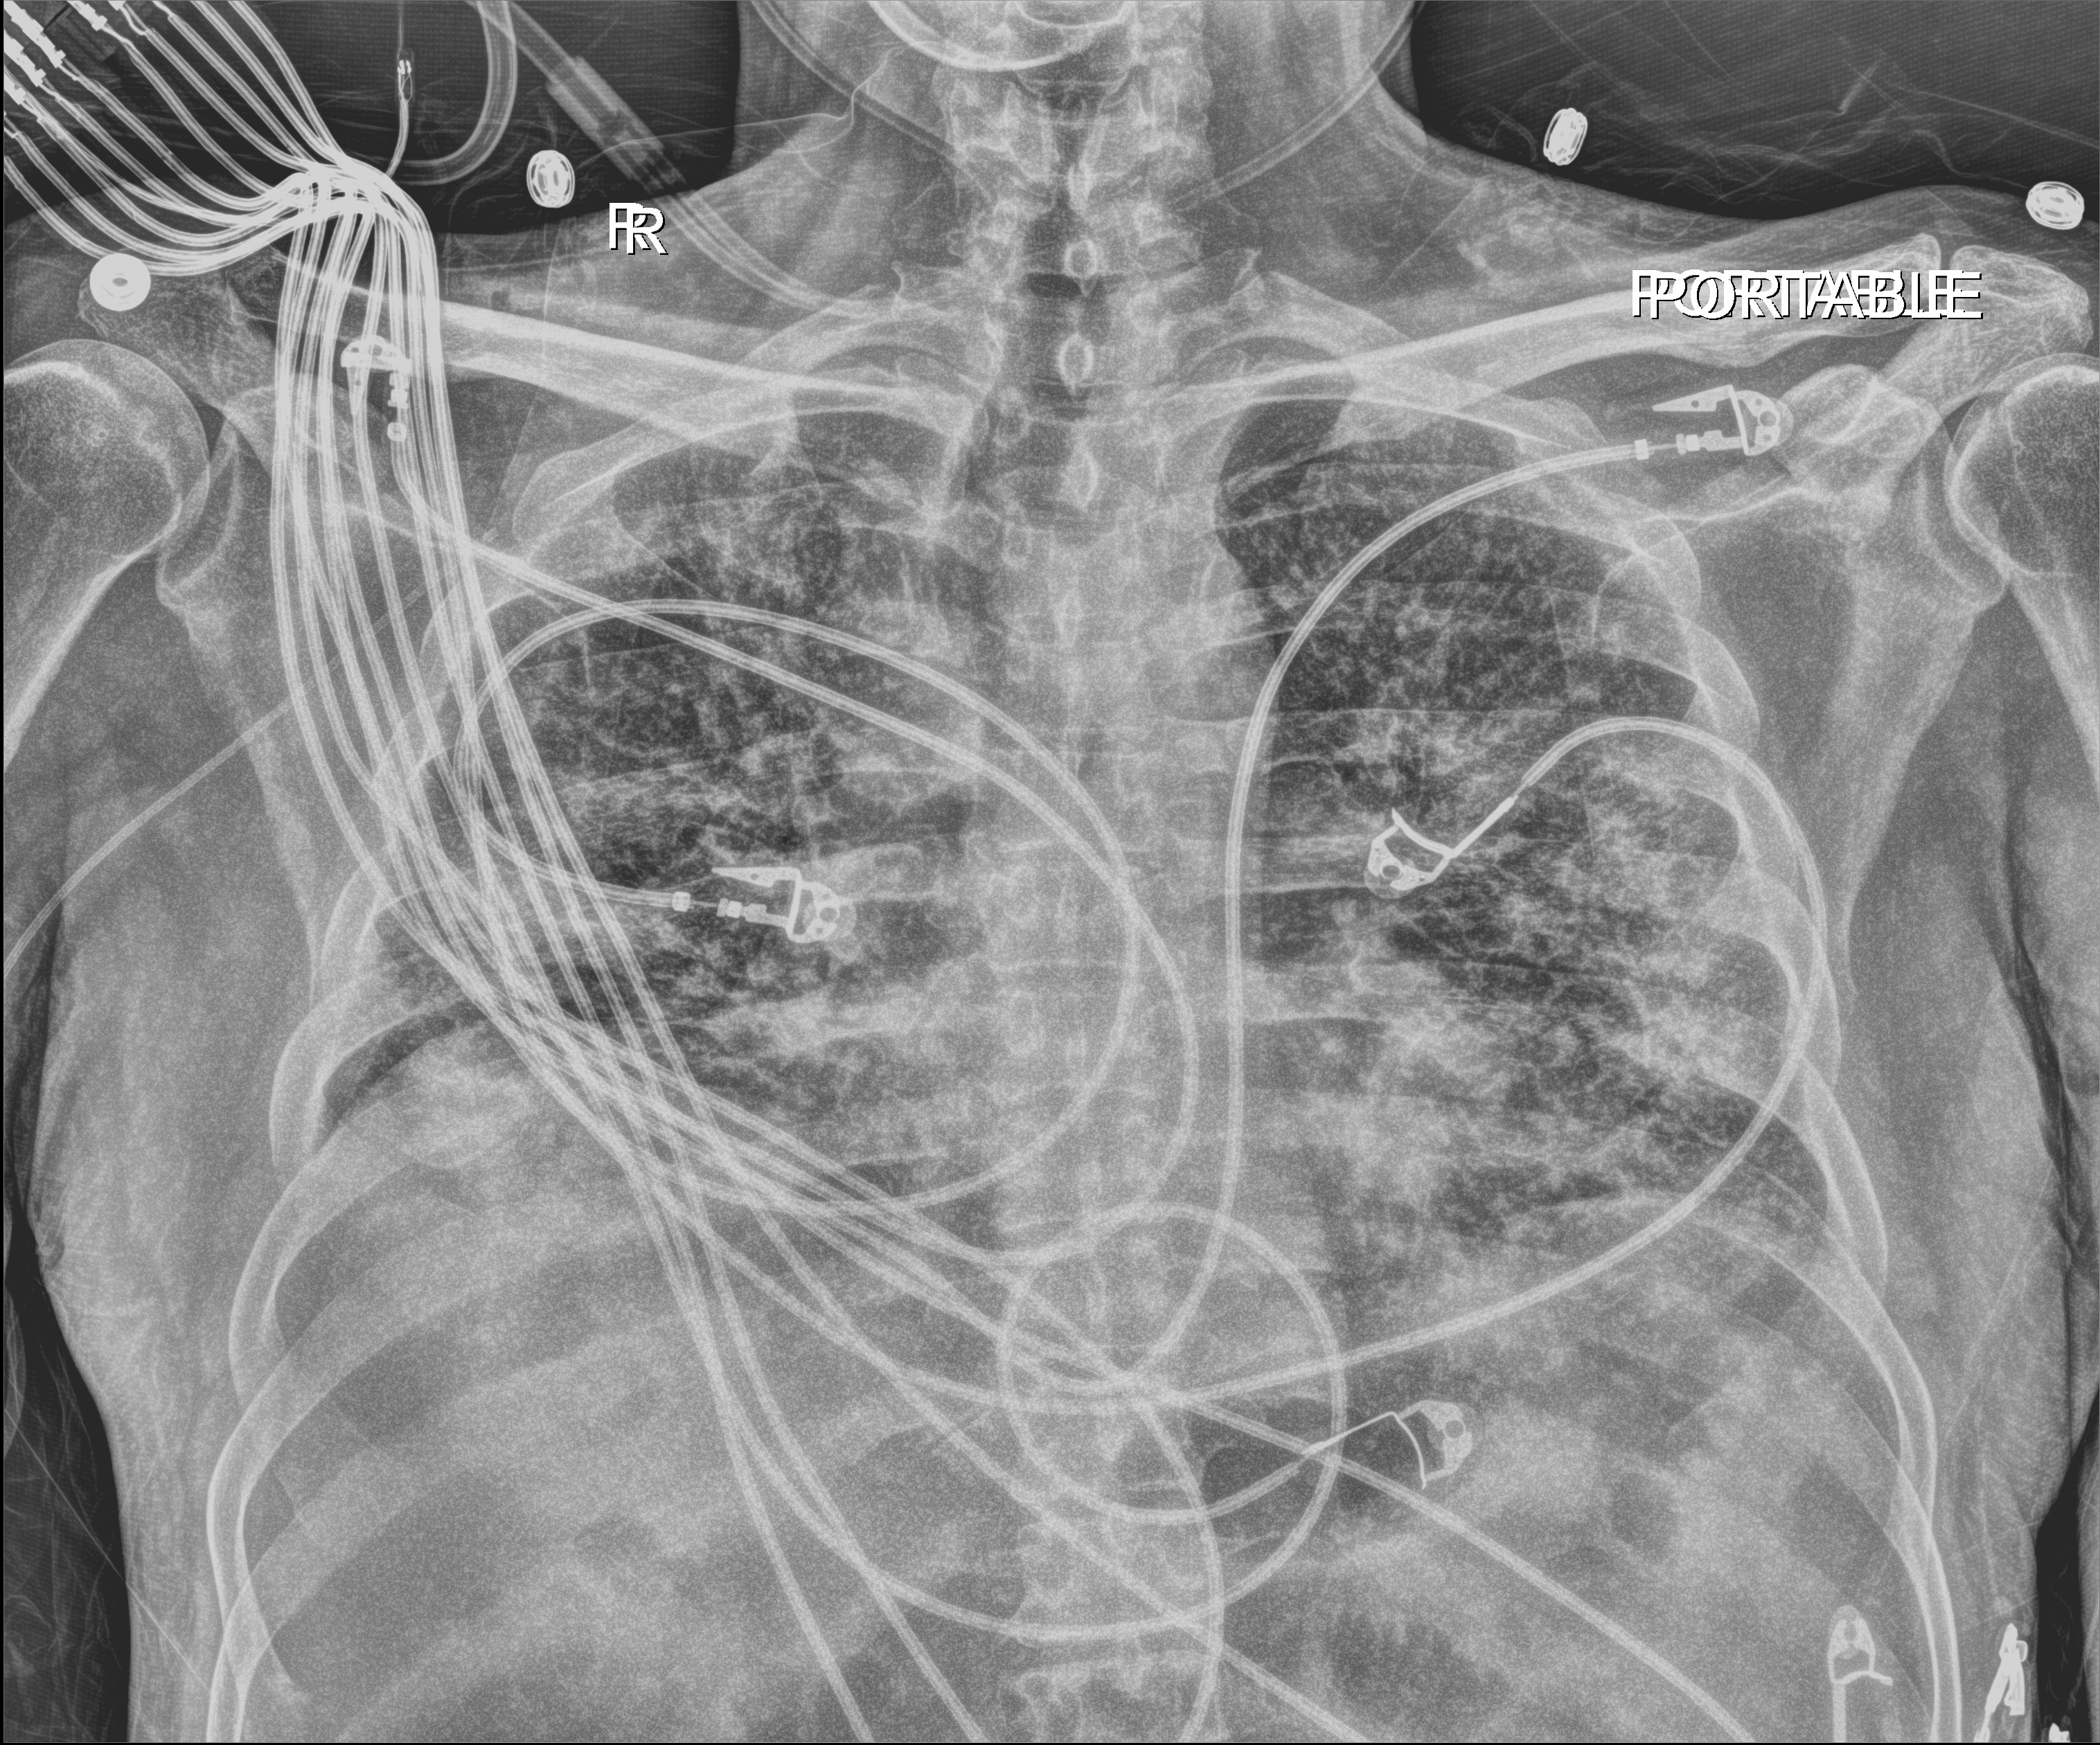
Bedside chest radiograph (digital radiography); anteroposterior (AP) projection. Patient hospitalised with COVID-19; male, aged 18–59 years.
Admission-level facts for this patient (not findings on this image; timing relative to this image not recorded): mechanically ventilated during this hospital stay: yes; admitted to intensive care during this hospital stay: yes.